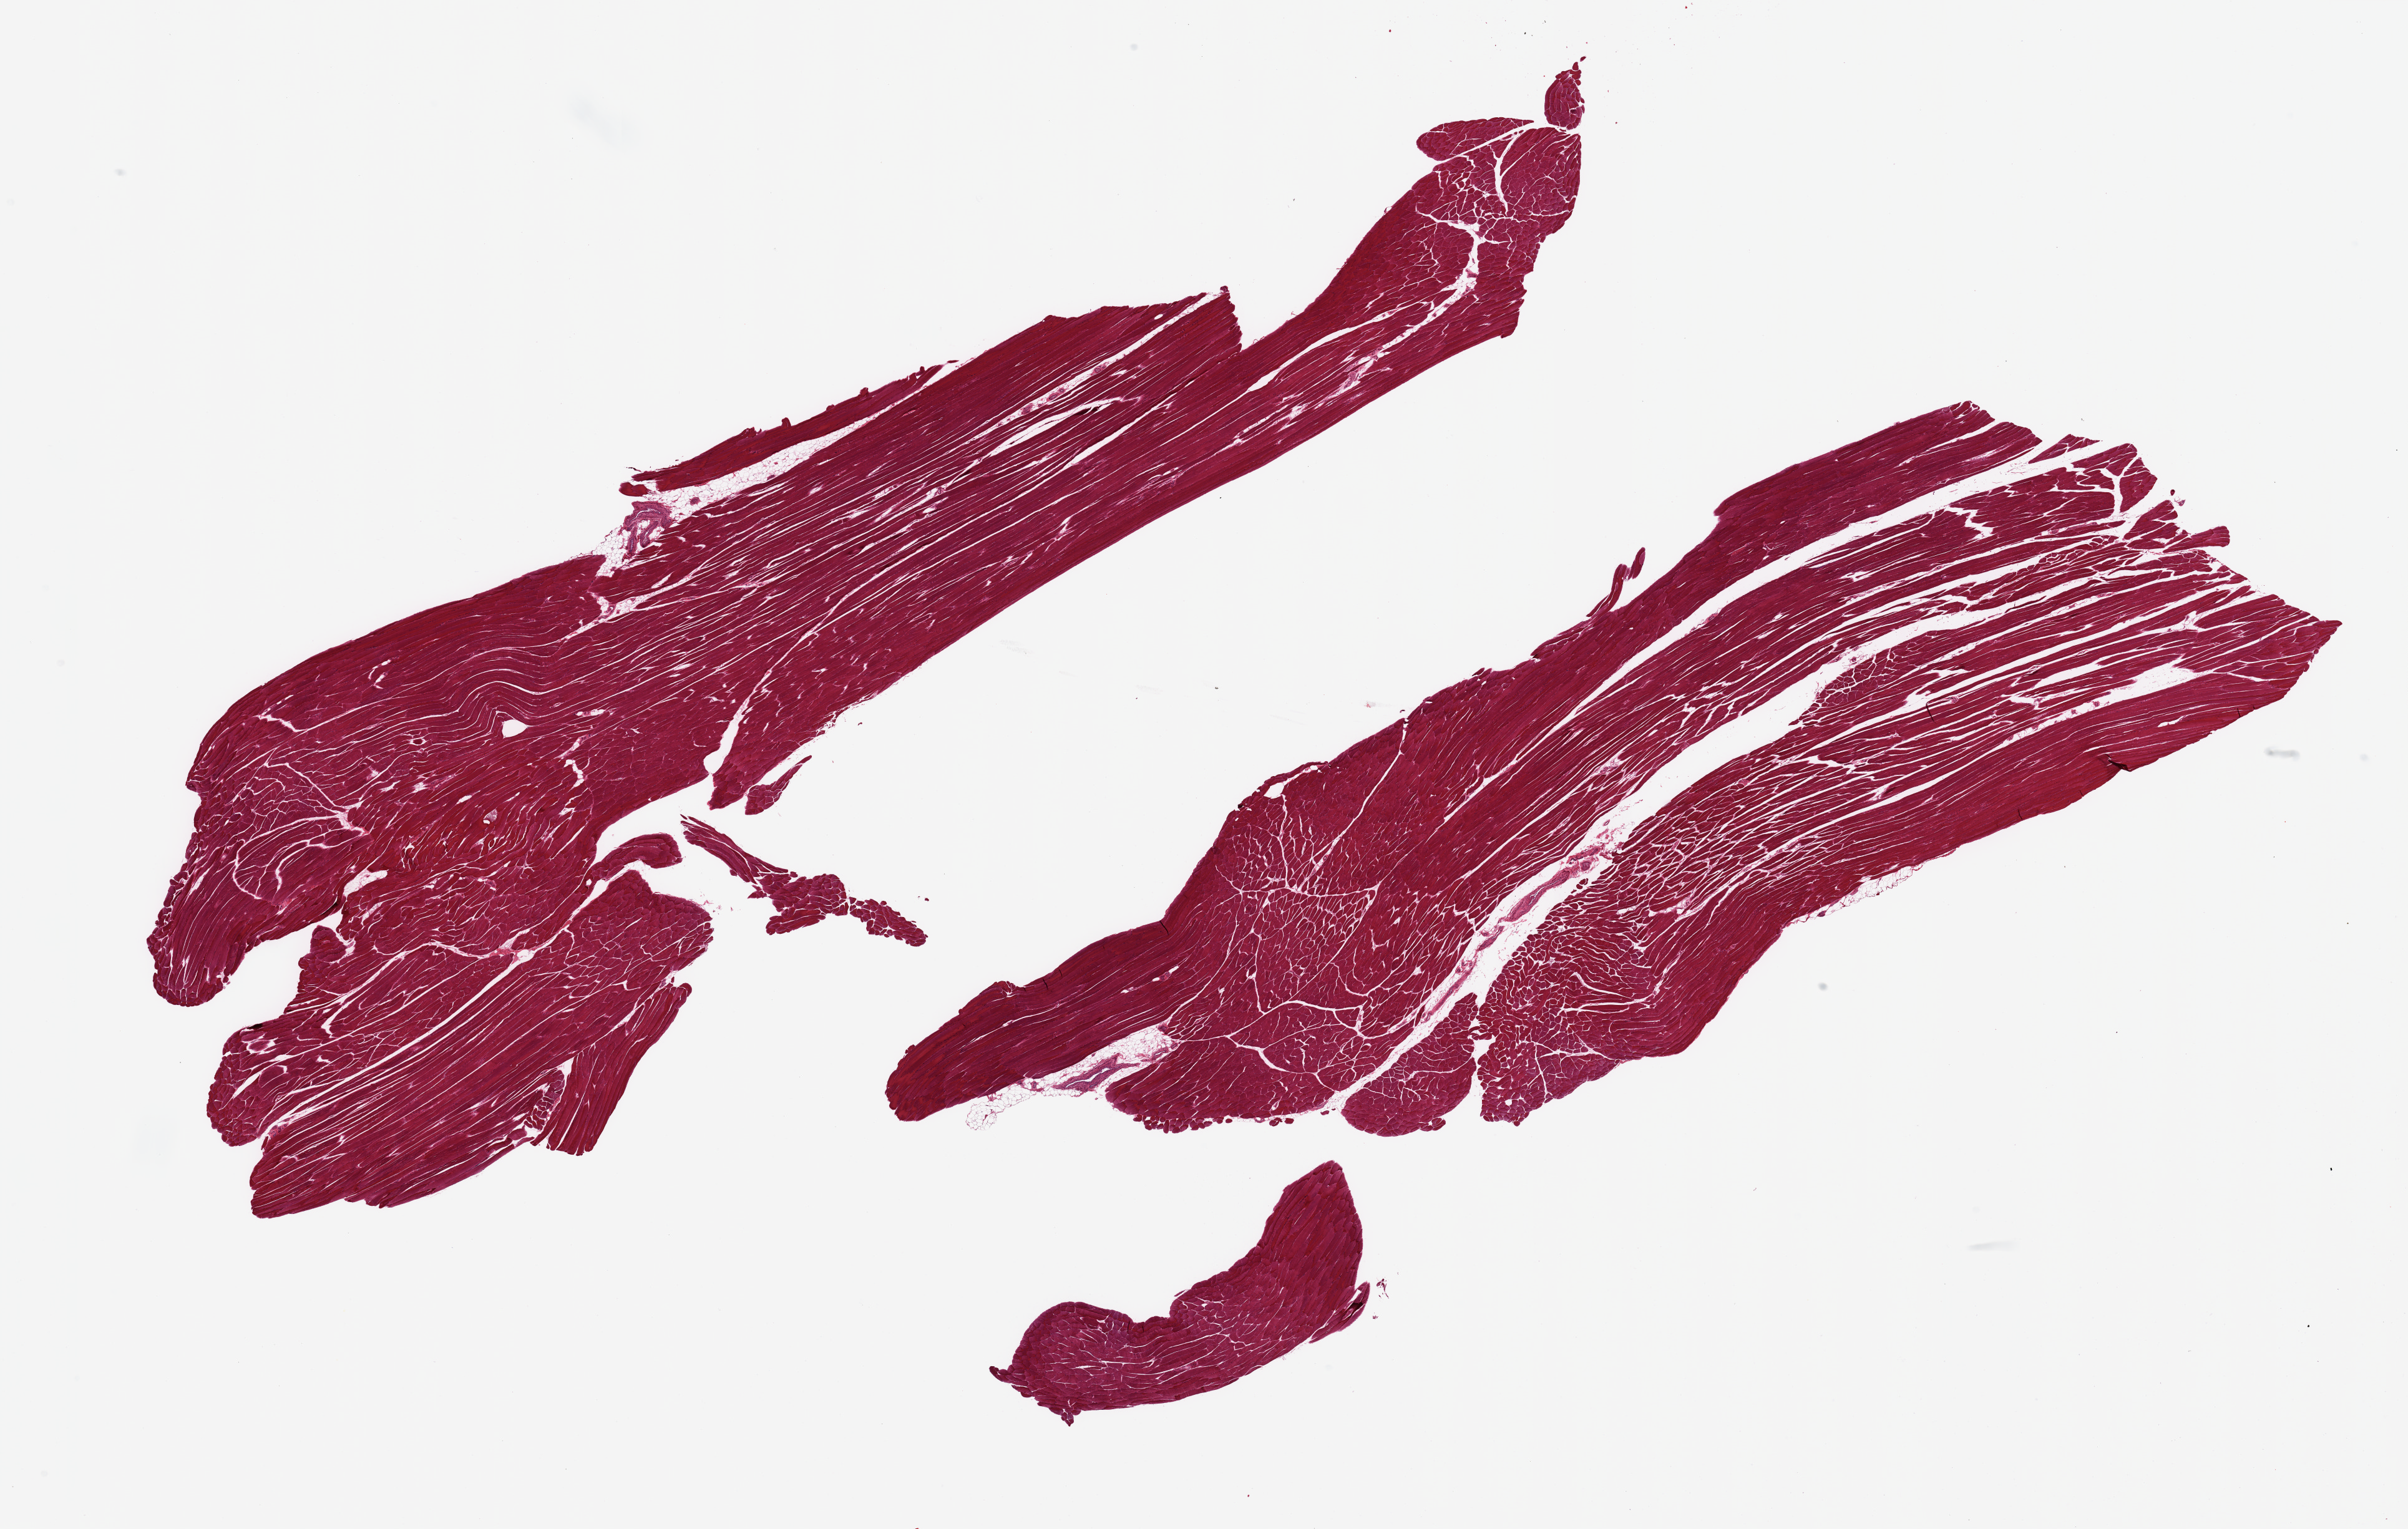
Hematoxylin and eosin (H&E) whole-slide image — whole scanned area (about 30.5 x 19.4 mm) shown as a low-resolution overview; PAXgene-fixed paraffin-embedded (PFPE) section; target tissue: skeletal muscle; tissue donor sample. Donor: male.
Pathologist's review note for this sample: 2 pieces; ~5% internal fat.